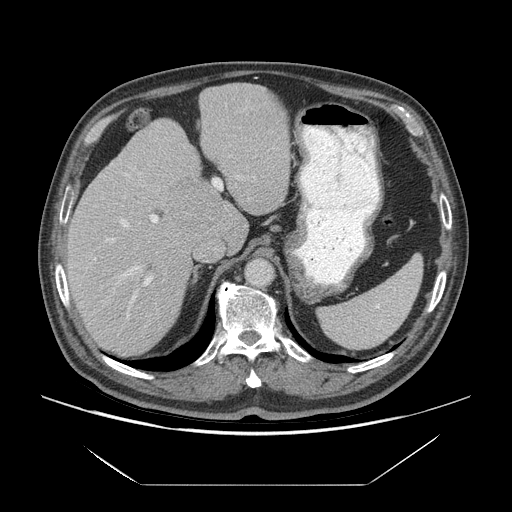
Contrast-enhanced abdominal CT (liver protocol), one axial slice; position 46 of 75 along the scan axis; reconstruction kernel STANDARD; 140 kVp; soft-tissue window (W 400 / L 40 HU); 512 × 512 image matrix. From the clinical record (not read from this slice): diagnosis: hepatocellular carcinoma (patient treated with transarterial chemoembolisation; whether this scan precedes or follows treatment is not stated here); TNM stage (as recorded): Stage-I; Child-Pugh class: A.
Annotated regions visible in this slice (semi-automatically segmented with operator editing):
- liver parenchyma outside the tumour (the mass and vessels are separate outlines, so this box may not span the whole liver): box from (x=66, y=84) to (x=290, y=356) px
- mass: (x=169, y=177)–(x=223, y=233)
- liver vessels: (x=94, y=169)–(x=255, y=304)